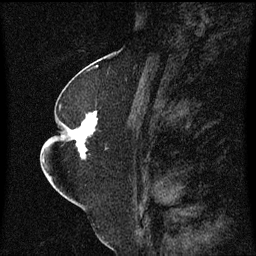
Breast MRI (dynamic contrast-enhanced), one sagittal slice; slice 31 of 60 in the series (ordered by position); dynamic contrast-enhanced series, image 2 of 3 at this slice position (ordered by acquisition); 1.5 T; TE 4.2 ms, TR 8.4 ms; 256 × 256 image matrix, field of view 200 × 200 mm. Female patient, age 52 years. From the clinical record (not read from this slice): setting: breast cancer imaged before/during neoadjuvant chemotherapy; receptor status: HR-positive, HER2-negative.
Annotated regions visible in this slice (semi-automatically segmented with operator editing):
- analysis volume of interest (the breast-tissue region the enhancement analysis was run in; not a lesion): bounding box <64,106,109,159> (left, top, right, bottom; pixels)
- tumour enhancement mask (voxels above the 70 % enhancement threshold inside the analysis volume of interest): <73,112,98,159>